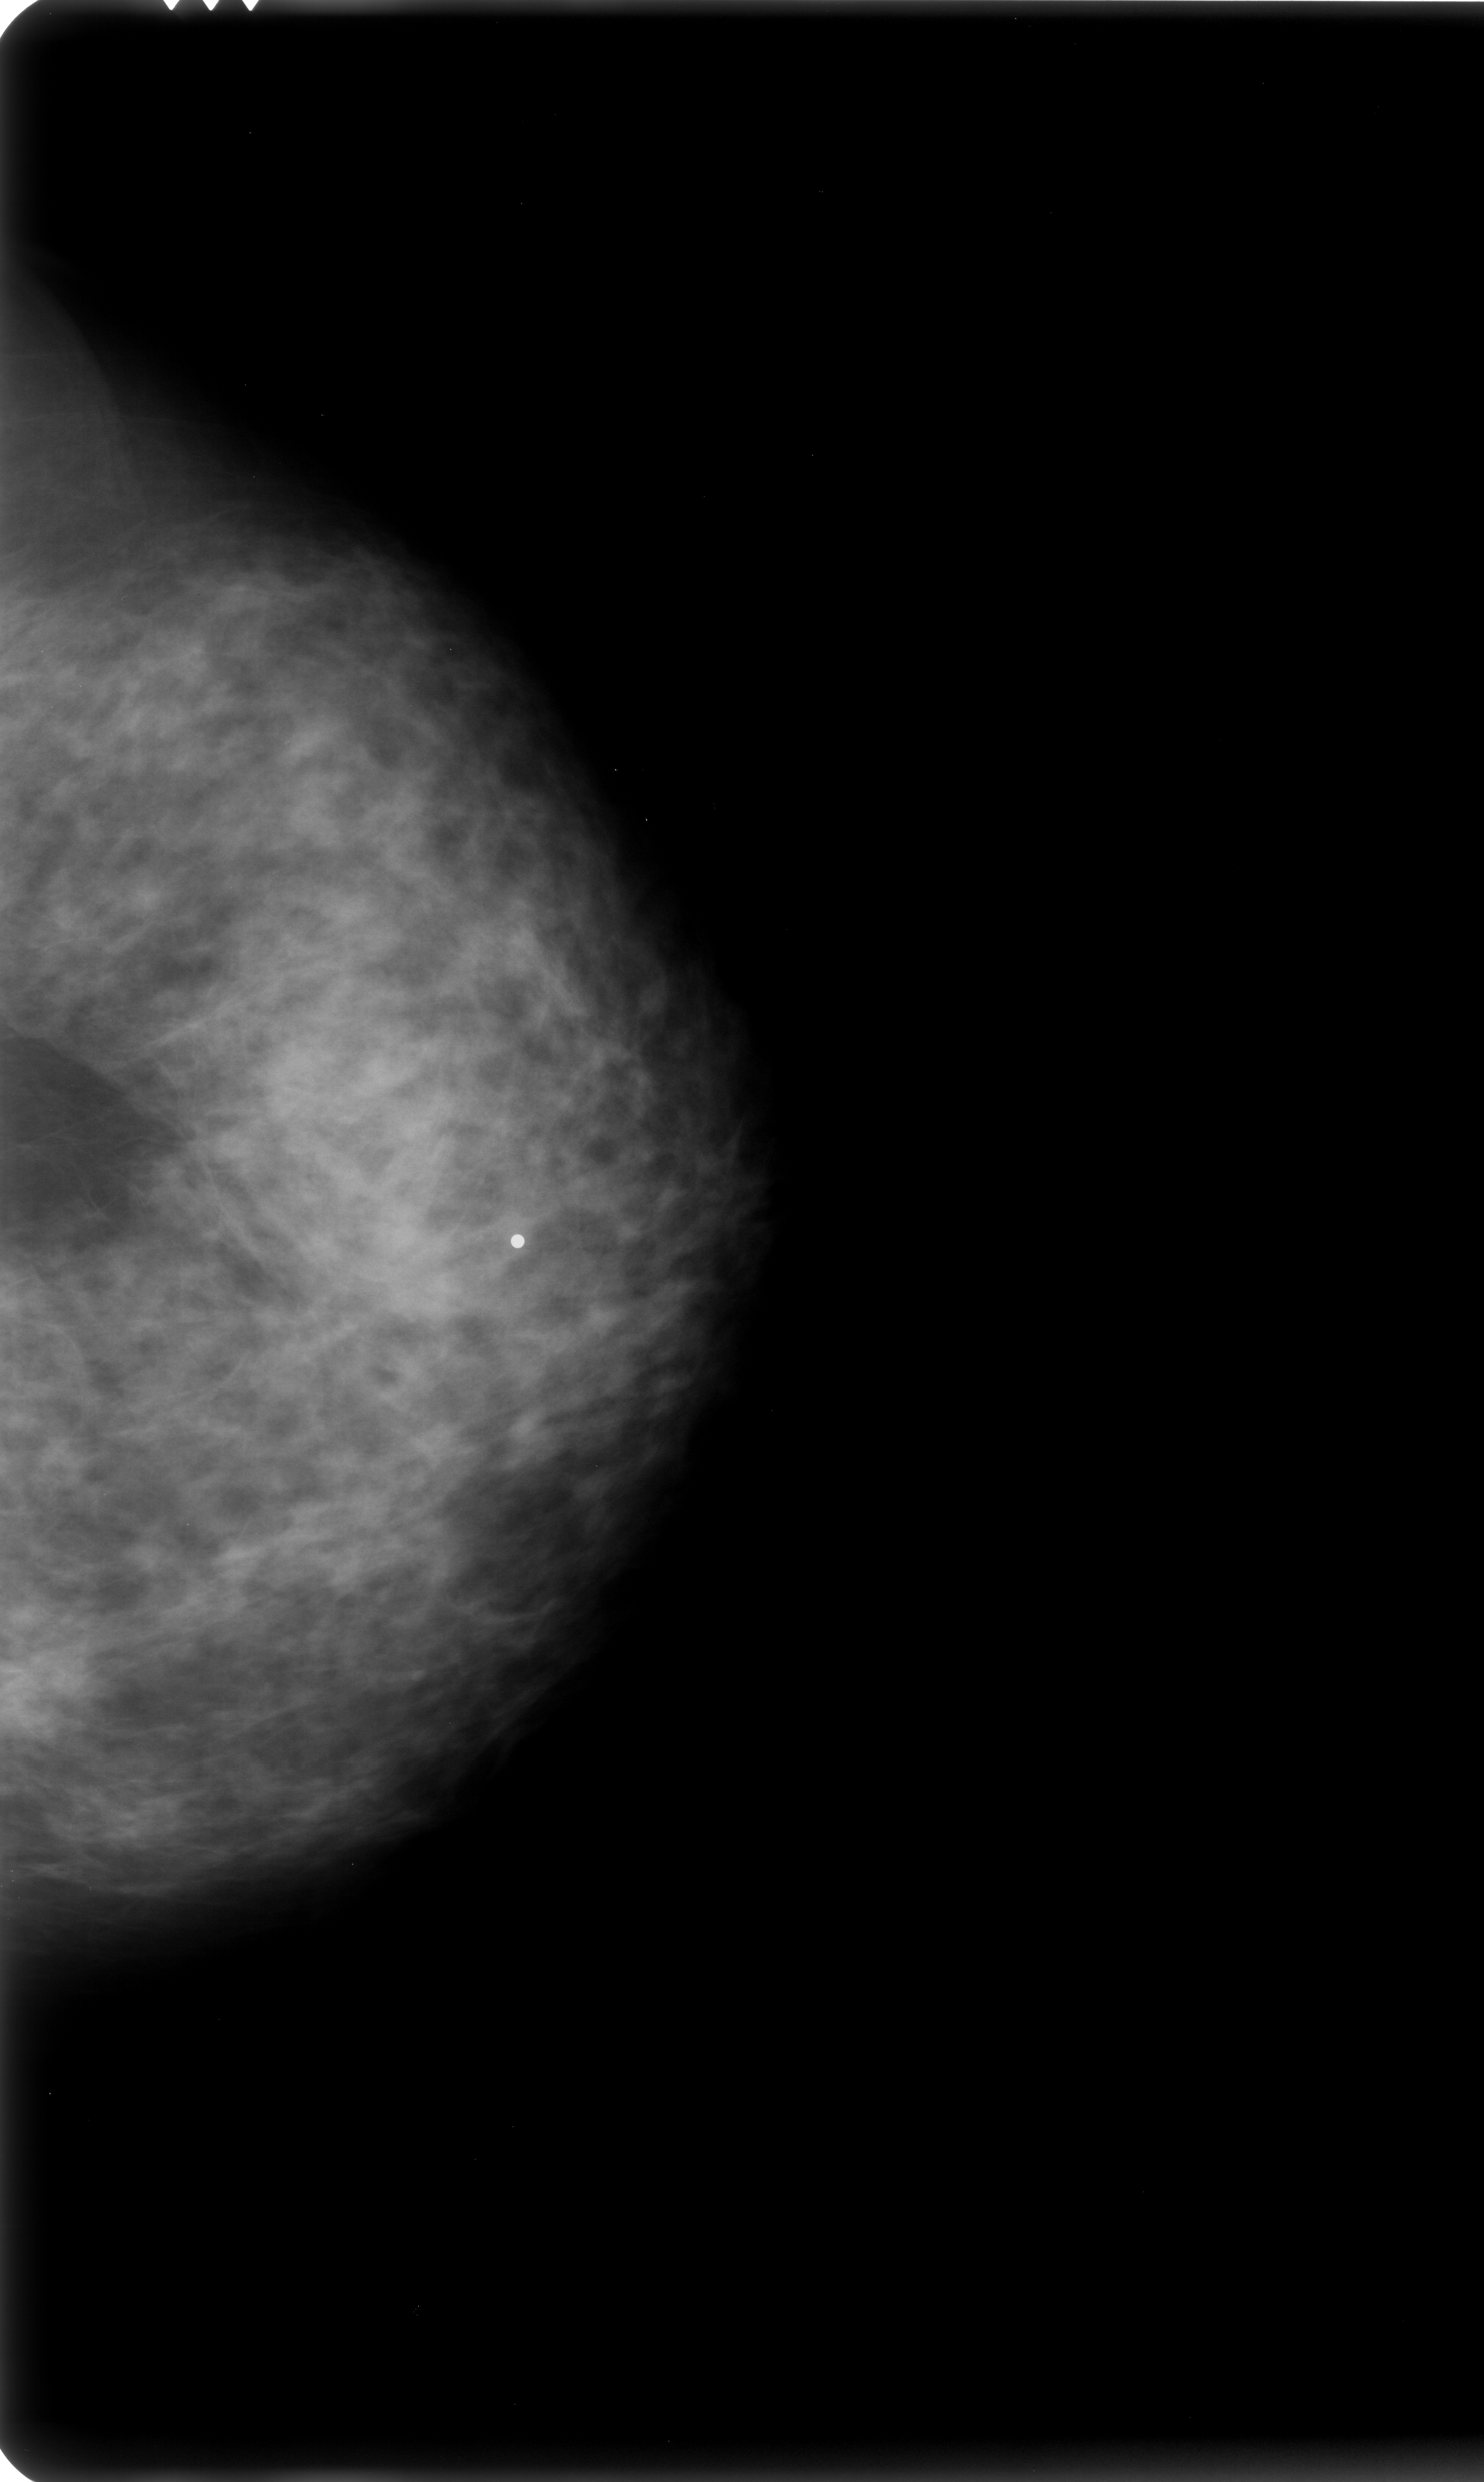
Scanned film-screen mammogram; left breast; craniocaudal (CC) view; 1484 × 2482 image matrix.
Expert-marked regions of interest on this film, with their recorded descriptors:
- mass, shape architectural distortion, margins ill defined; BI-RADS assessment category 4; subtlety rating 2 on a 1 (subtle) to 5 (obvious) scale; pathology (as recorded): malignant: bounding box (x1, y1, x2, y2) in pixels: (233, 1123, 534, 1364)